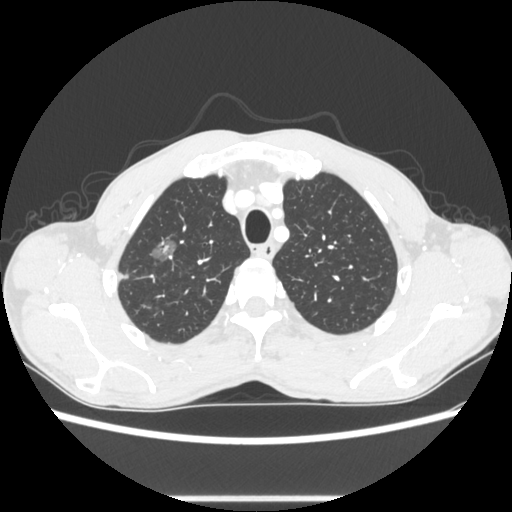
Chest CT, one axial slice. Slice 234 of 289 in the series (ordered by position). Lung window (W 1500 / L -600 HU). 1.25 mm slice thickness. 512 × 512 image matrix, field of view 350 × 350 mm. Patient: male, 54 years. From the clinical record (not read from this slice): clinical TNM (as recorded): T1a N0 M0.
Outlined on this slice (bounding box drawn by a radiologist):
- lung tumour (recorded histology: adenocarcinoma): bounding box <144,230,182,267> (left, top, right, bottom; pixels)